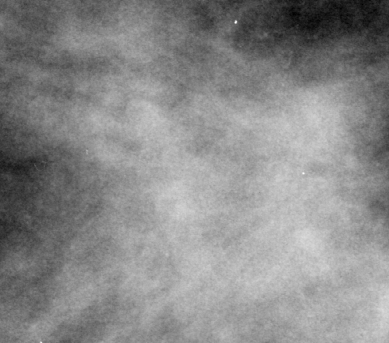
Cropped region of a digitized screen-film mammogram centred on a radiologist-marked abnormality, right breast, MLO view, BI-RADS breast density category 3 (scale 1–4).
Marked abnormality: mass, shape irregular, margins spiculated; BI-RADS assessment category 4; subtlety rating 3 on a 1 (subtle) to 5 (obvious) scale; pathology result (as recorded, not read from the image): malignant.